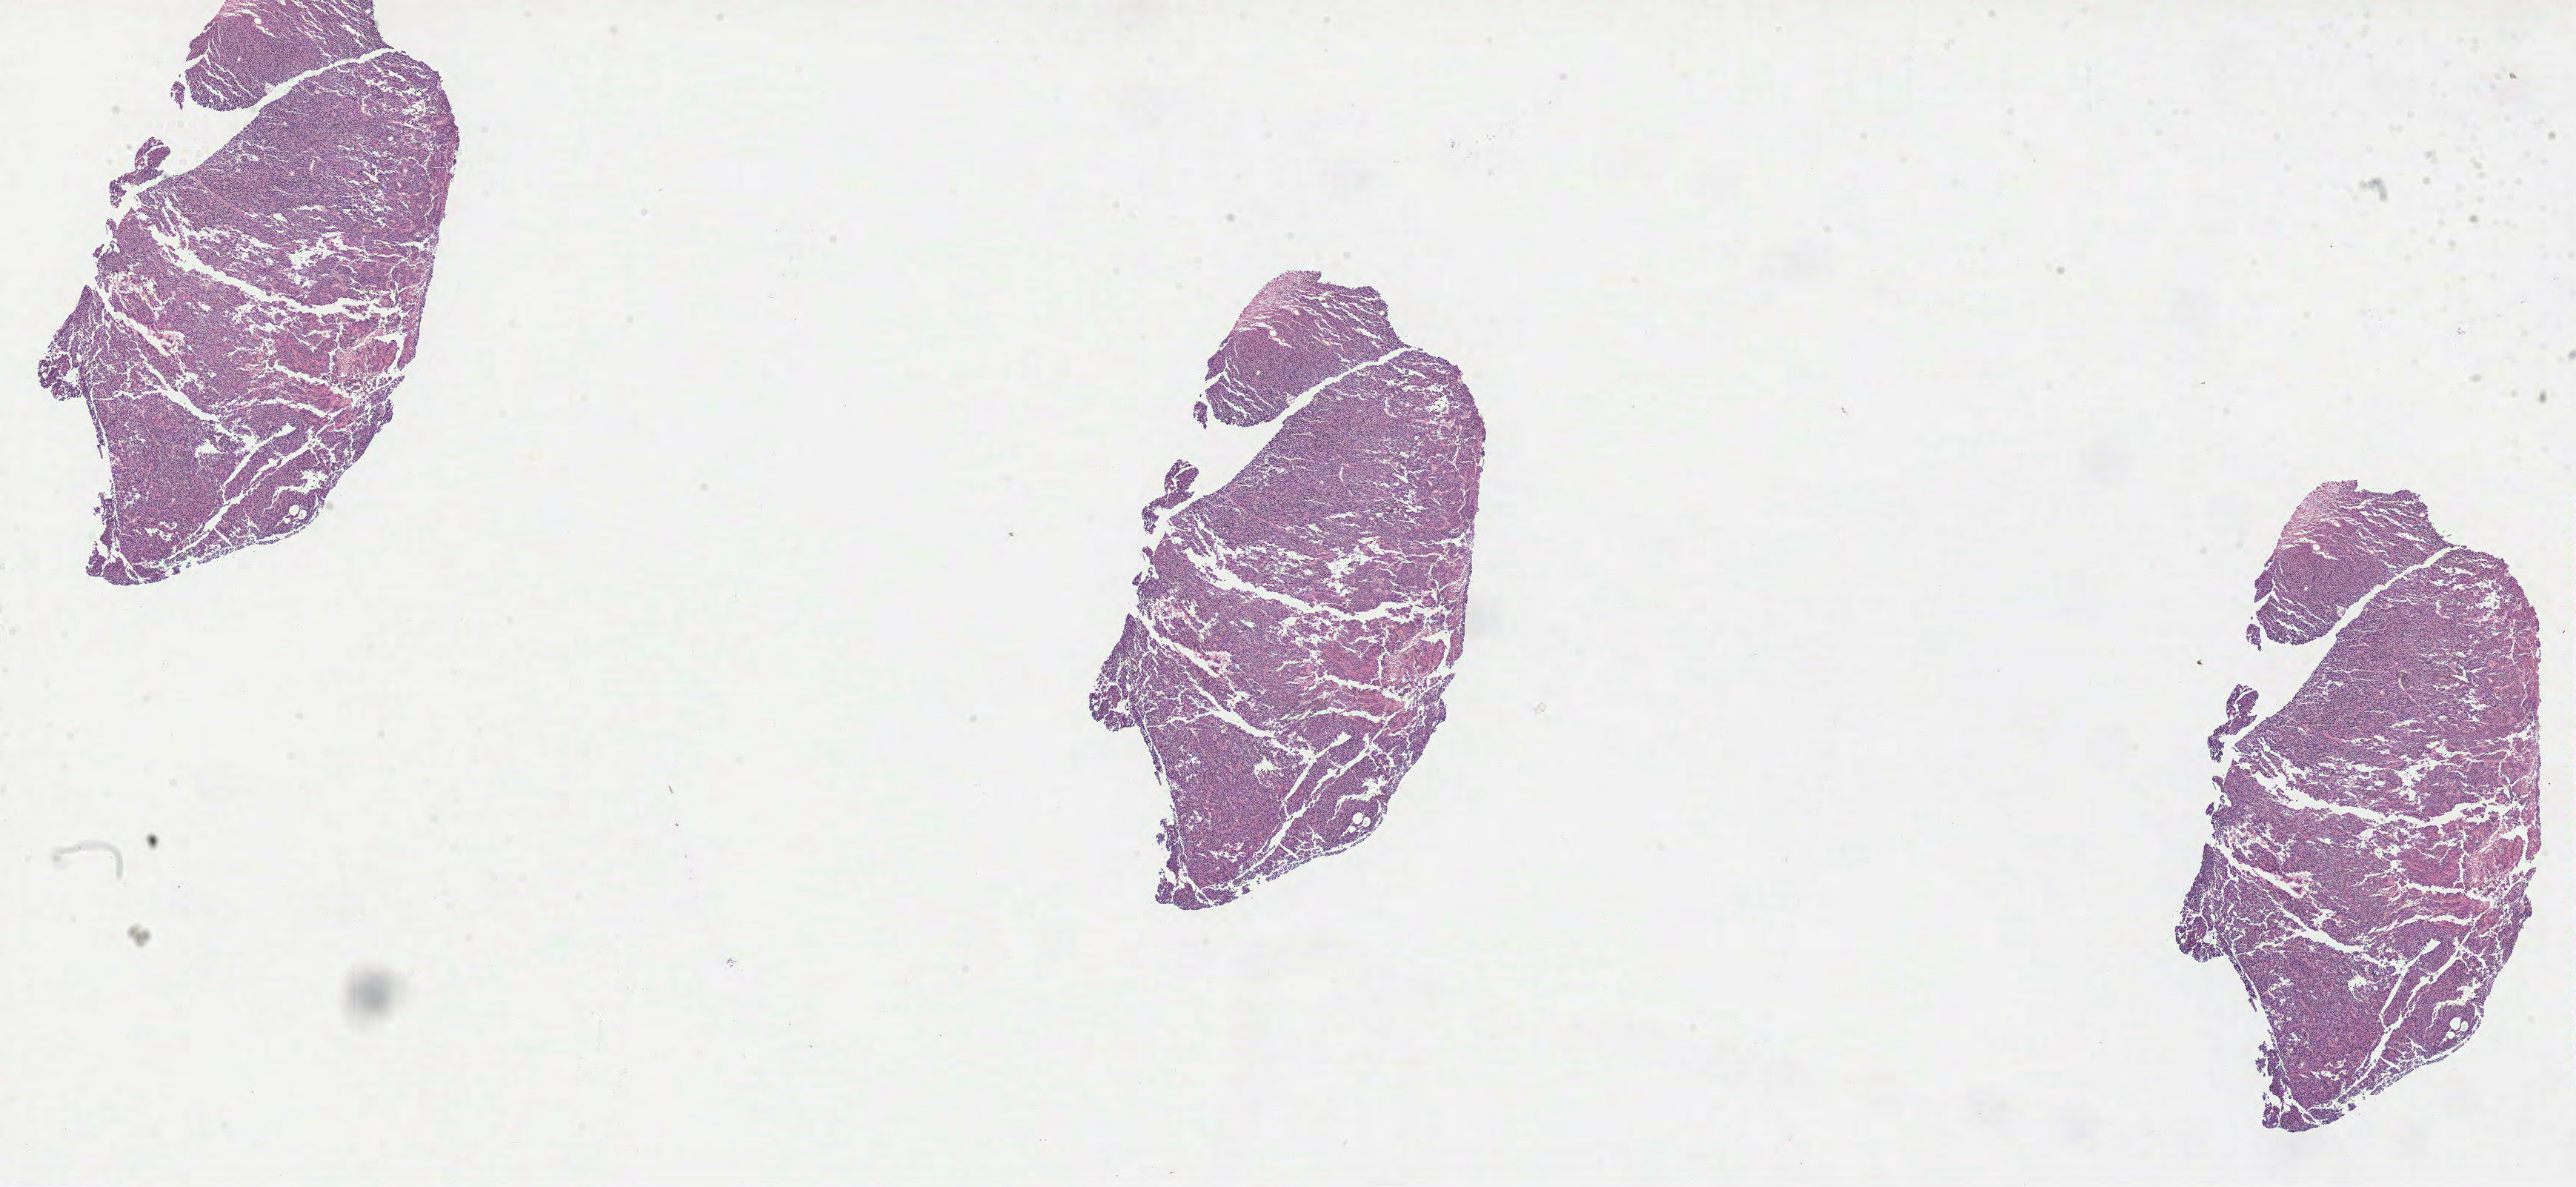
Hematoxylin and eosin (H&E) stained whole-slide image, whole scanned area (about 28.0 x 12.9 mm) shown as a low-resolution overview, formalin-fixed paraffin-embedded (FFPE) diagnostic section, primary tumour sample from the brain. Male, age 66 years at initial diagnosis. Histologic grade: G3 (poorly differentiated).
- diagnosis: Oligodendroglioma, anaplastic (cerebrum)
- laterality: left